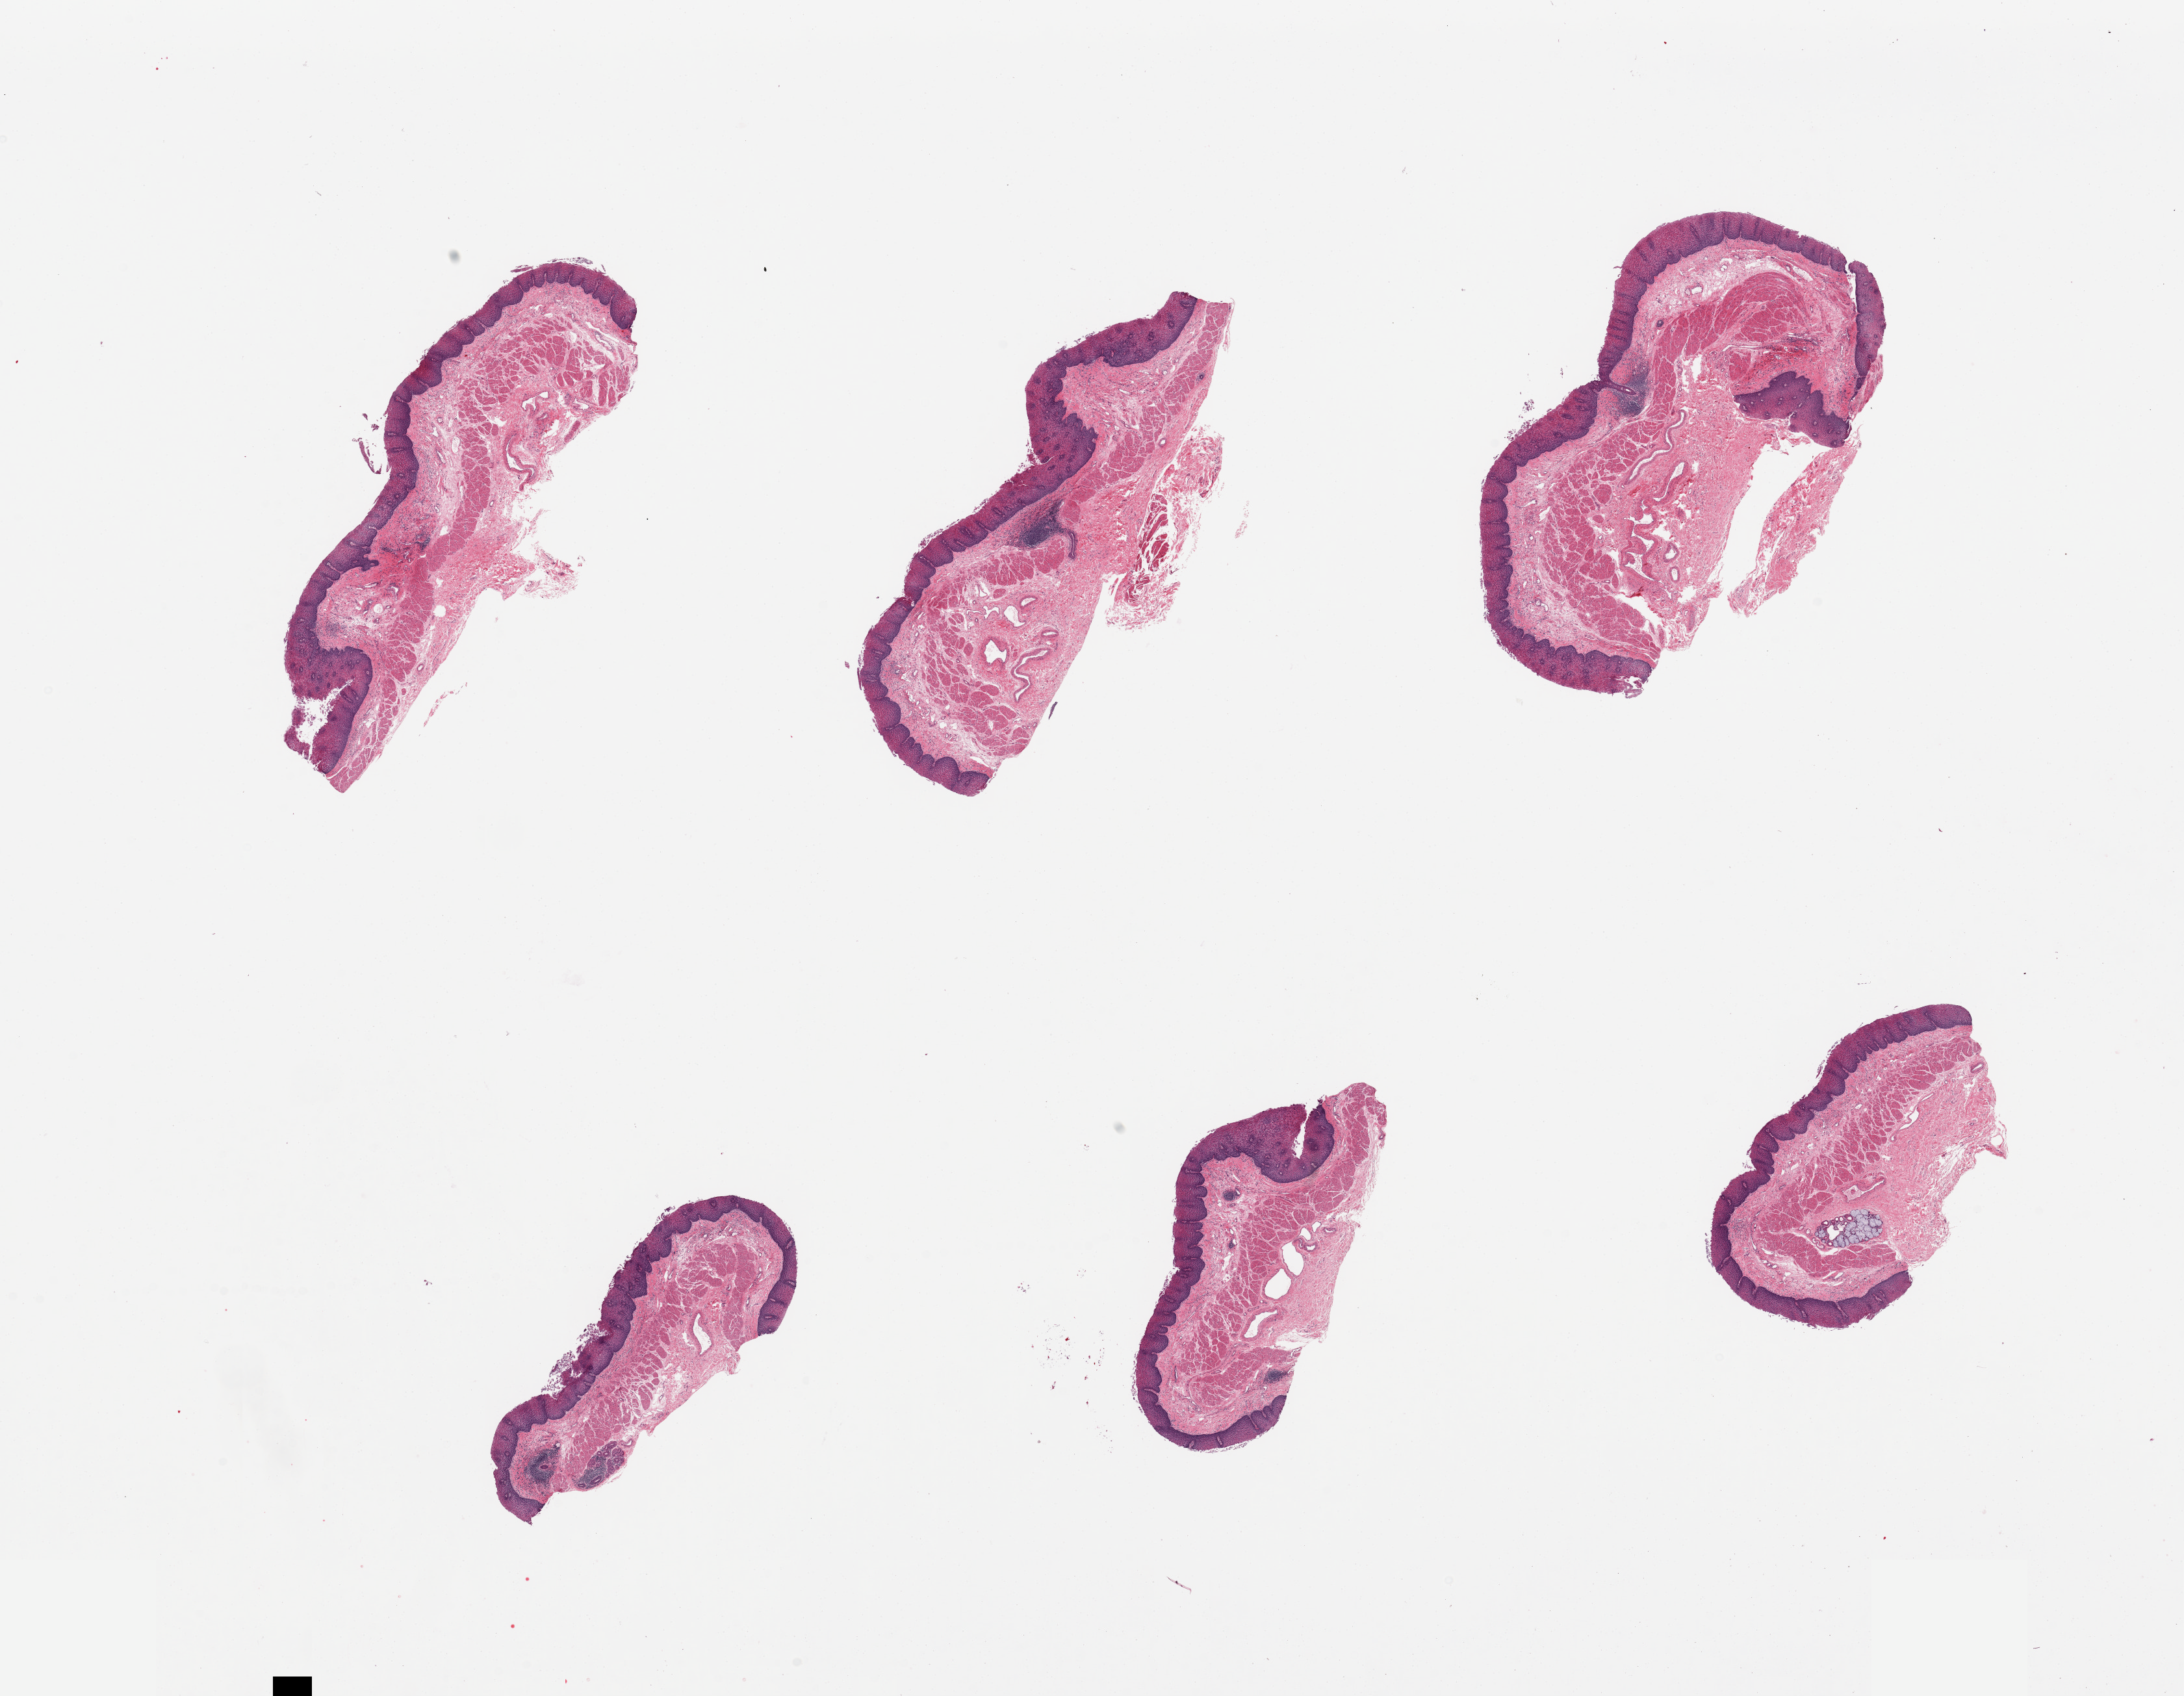
Digitized hematoxylin and eosin (H&E)-stained section, brightfield — a low-resolution overview of the entire scanned area, about 26.6 x 20.6 mm (from a 20x scan). PAXgene-fixed paraffin-embedded (PFPE) section. Section of esophageal mucous membrane (target tissue). Donor tissue sample. Female donor.
Reviewer comment on this tissue sample: 6 pieces, squamous mucosa 0.25mm; focal submucosal glands.